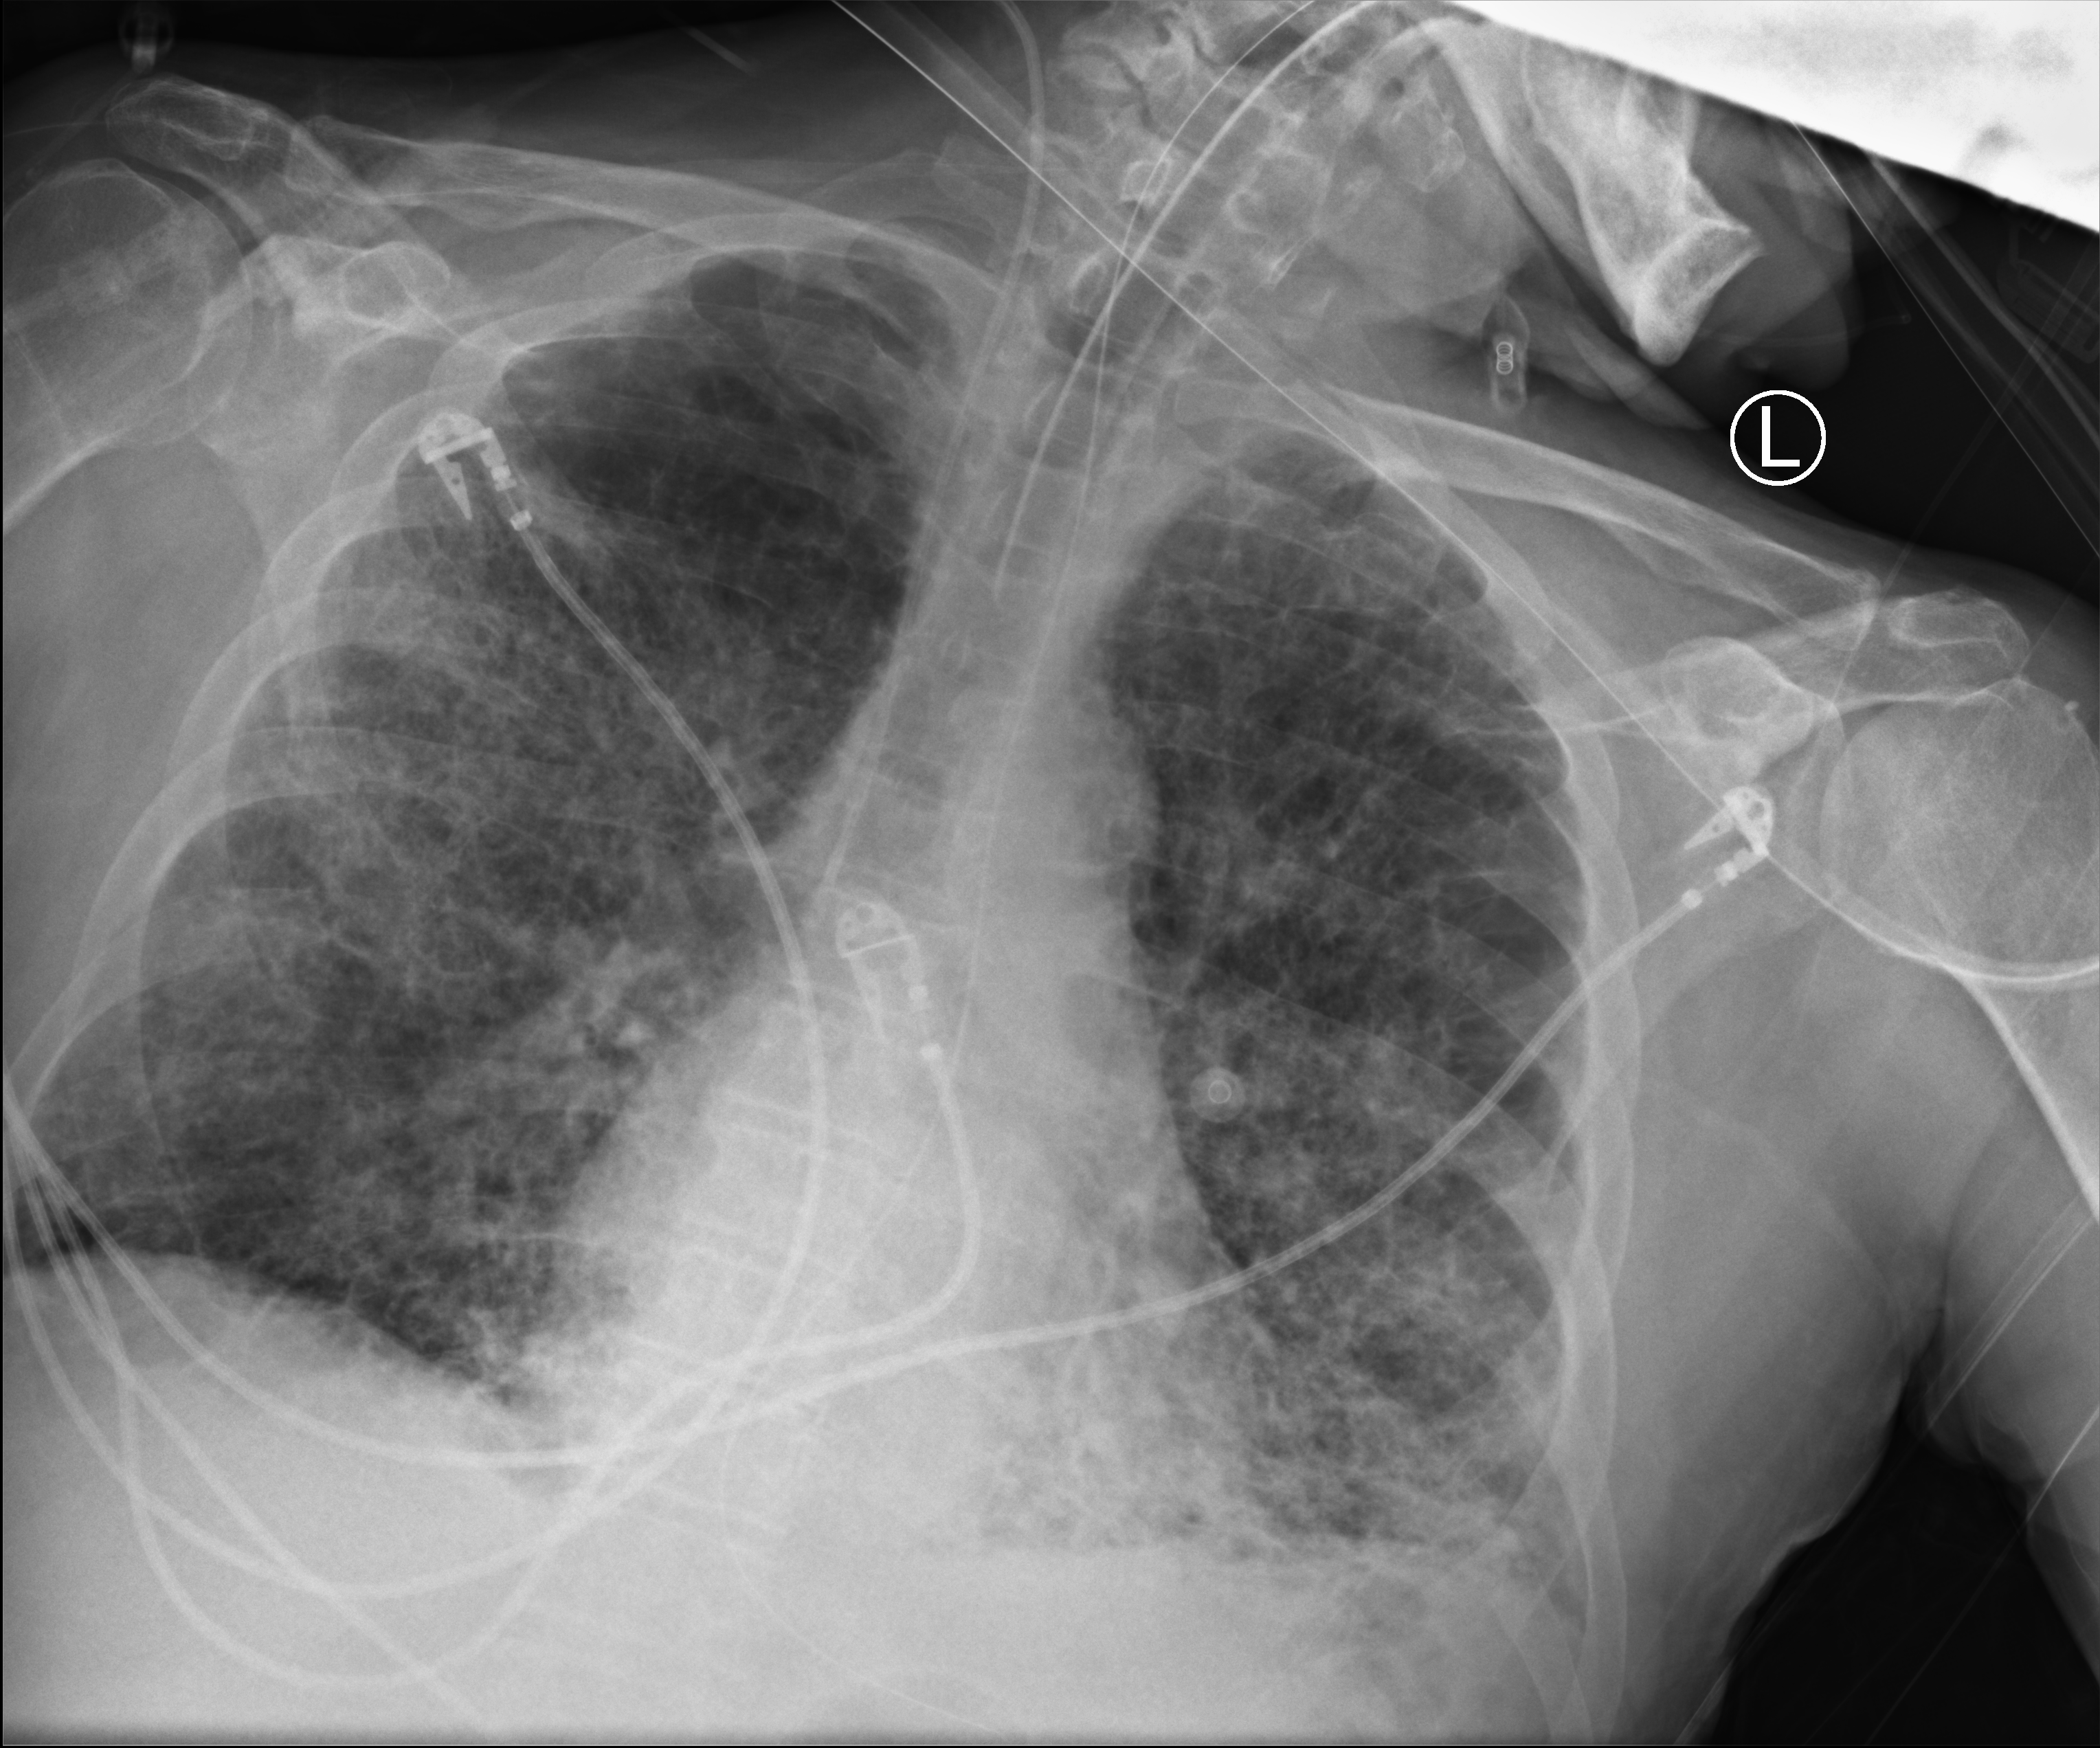
Portable chest radiograph, anteroposterior (AP) projection. Male patient hospitalised with COVID-19, age 75–90 years.
Admission-level facts for this patient (not findings on this image; timing relative to this image not recorded):
- mechanically ventilated during this hospital stay: yes
- admitted to intensive care during this hospital stay: yes